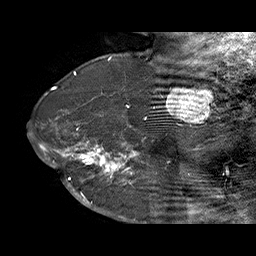
Breast MRI (dynamic contrast-enhanced), one sagittal slice. Slice 49 of 70 in the series (ordered by position). Dynamic contrast-enhanced series, time point 2 of 6 at this slice position (early post-contrast). 1.5 T. TE 4.5 ms, TR 32.4 ms. 3 mm slice thickness. 256 × 256 image matrix, field of view 180 × 180 mm. Female patient. From the clinical record (not read from this slice): setting: breast cancer imaged before/during neoadjuvant chemotherapy; receptor status: HR-positive, HER2-negative.
Structures marked on this image (semi-automatically segmented with operator editing):
- analysis volume of interest (the breast-tissue region the enhancement analysis was run in; not a lesion): box from (x=71, y=128) to (x=159, y=202) px
- tumour enhancement mask (voxels above the 100 % enhancement threshold inside the analysis volume of interest): (x=71, y=128)–(x=144, y=202)